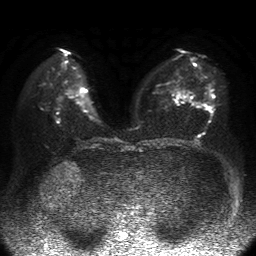
Breast MRI, one axial slice. Diffusion-weighted series; image 2 of 4 stored at this slice position (different b-values; order by instance number). 1.5 T. 4 mm slice thickness. 256 × 256 image matrix, field of view 360 × 360 mm. Female patient.
Outlined on this slice (manually delineated by an expert):
- tumour on diffusion-weighted imaging: bounding box [x1, y1, x2, y2] px = [206, 105, 212, 111]